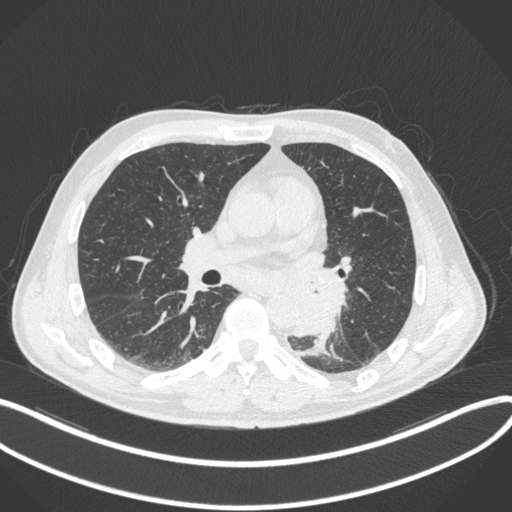
Chest CT, one axial slice. Position 177 of 328 along the scan axis. Reconstruction kernel B31f. 120 kVp. Lung window (W 1500 / L -600 HU). 1 mm slice thickness. 512 × 512 image matrix, field of view 400 × 400 mm. Male patient, age 59 years. Case-level facts recorded for this patient, not image findings: clinical TNM (as recorded): T2a N2 M0.
Outlined on this slice (rectangle marked by the reading radiologist):
- lung tumour (recorded histology: squamous cell carcinoma): box from (x=290, y=268) to (x=350, y=340) px